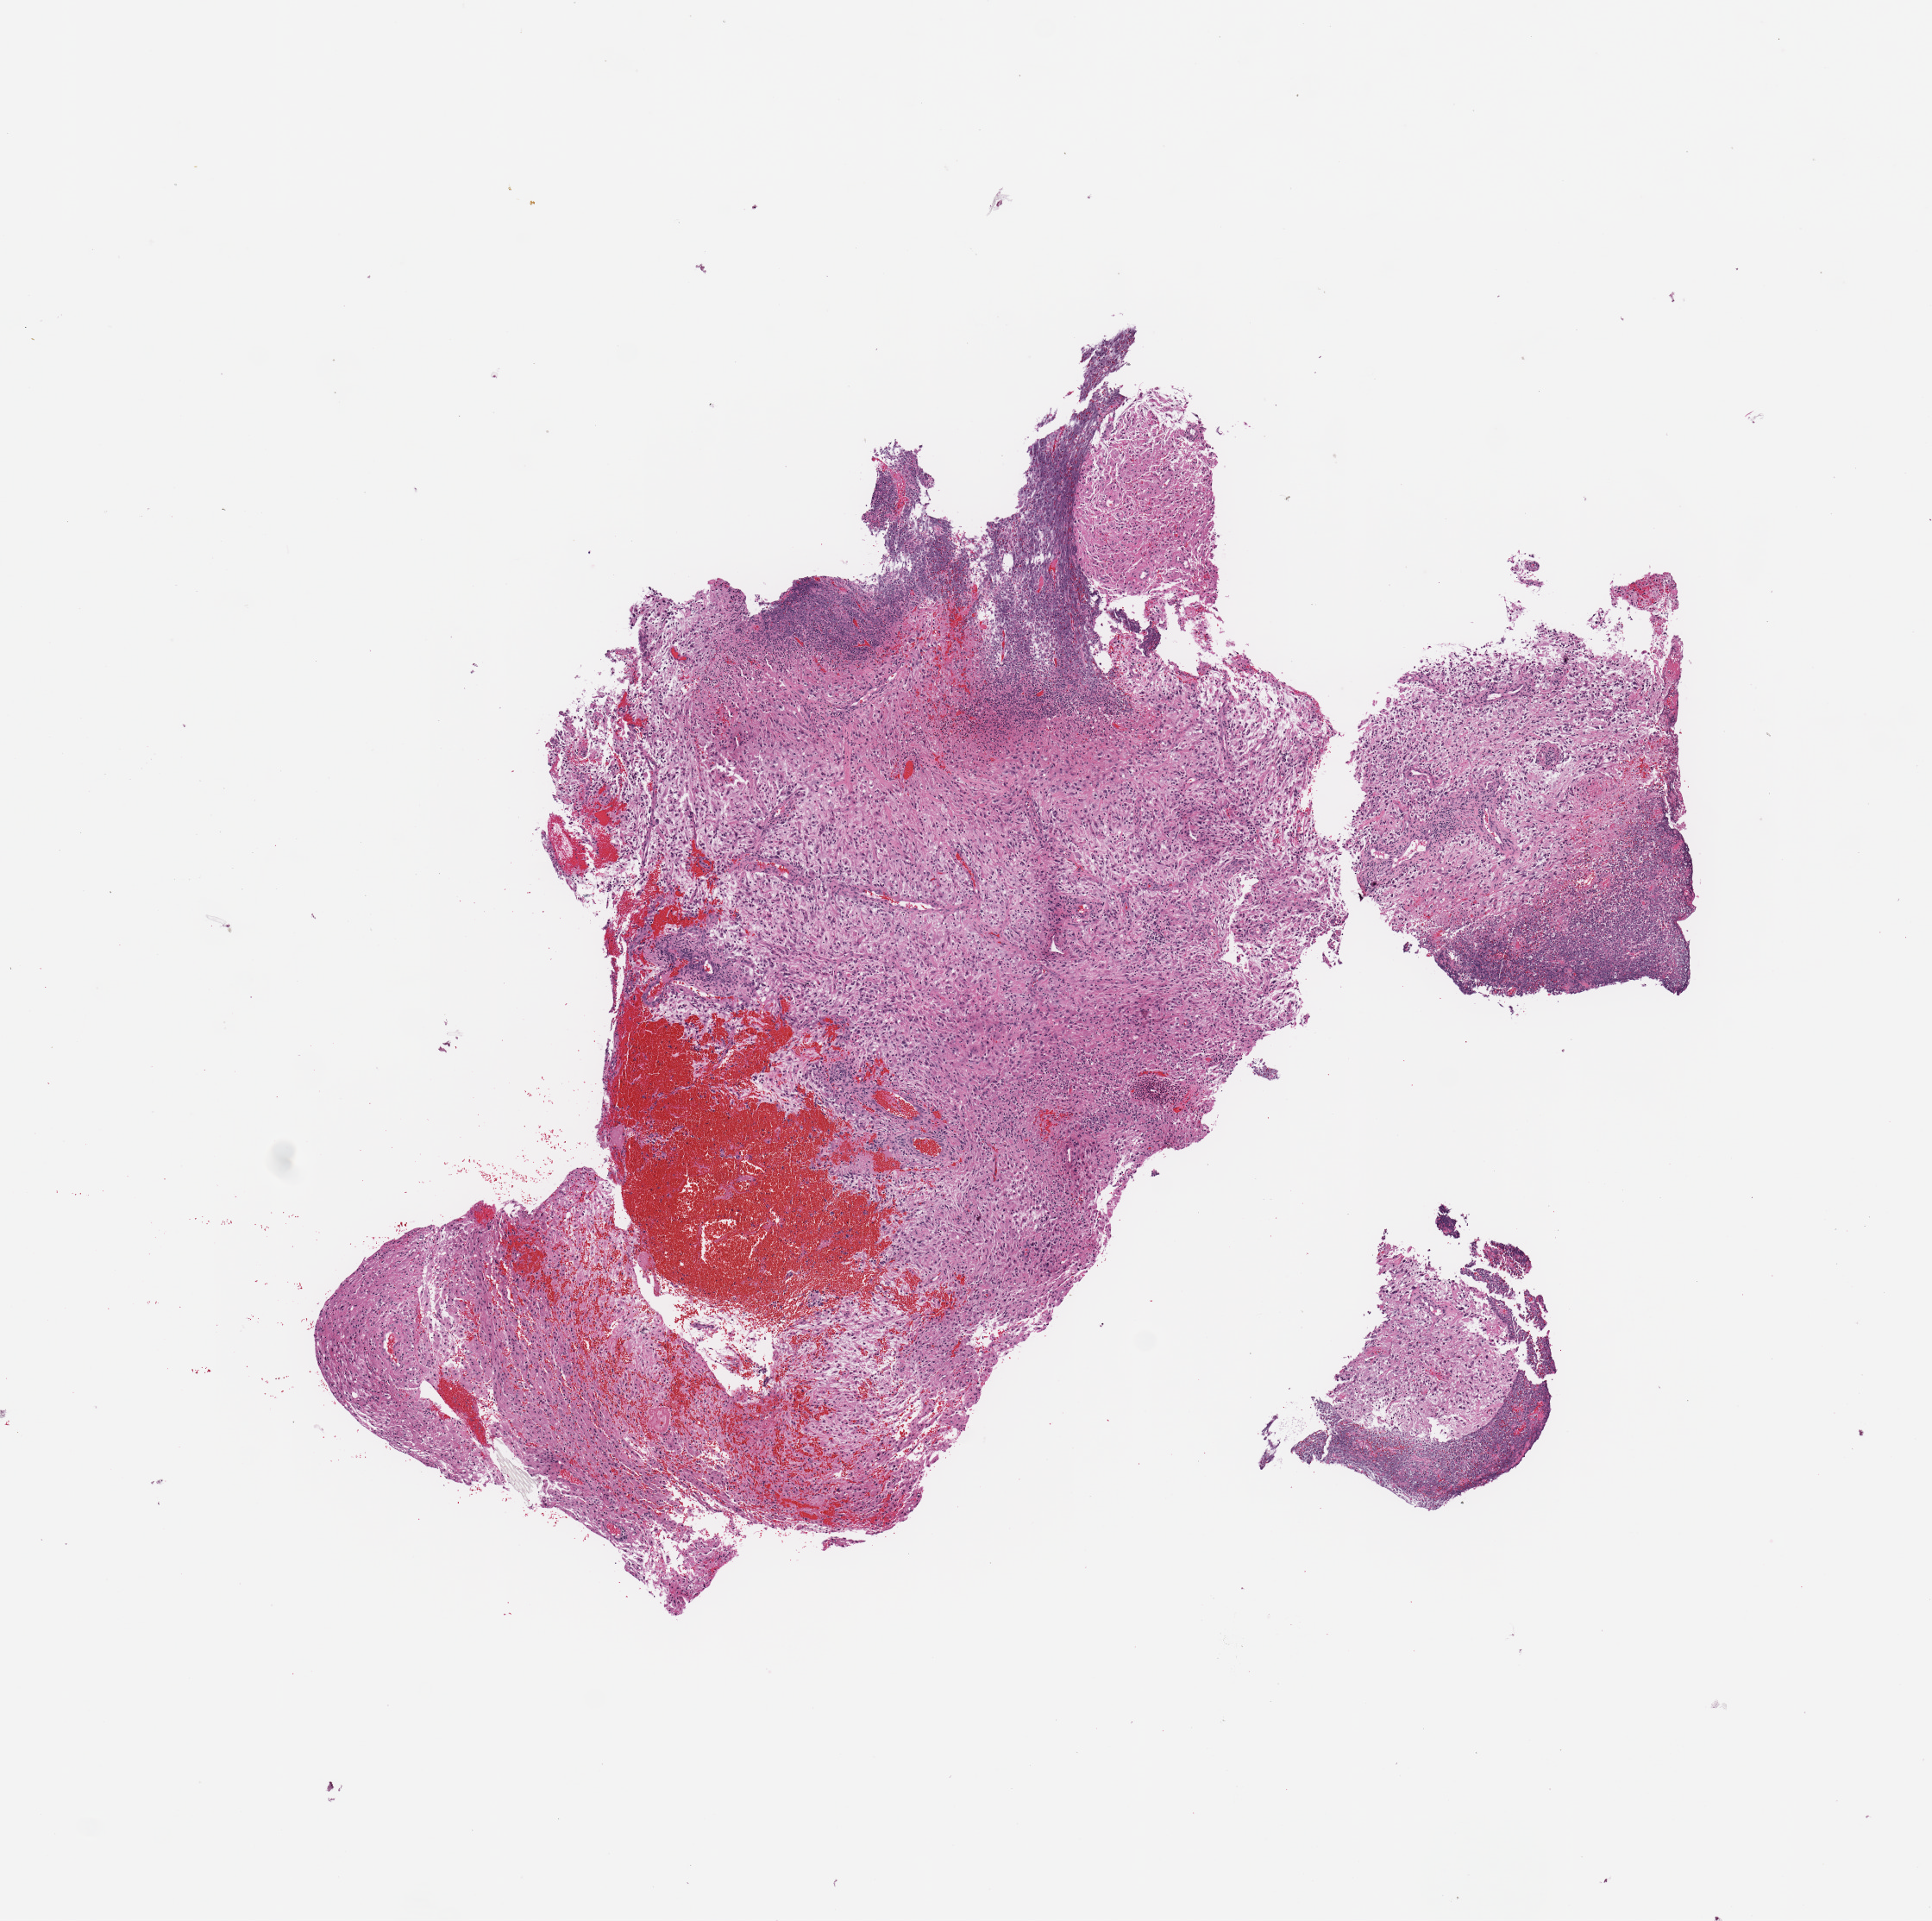
H&E-stained whole-slide image — low-resolution overview of the scanned area, about 8.9 x 8.8 mm (slide scanned at 20x). Tumour tissue sample, sampled site: brain. Female, 50 y/o. Slide review estimates, as recorded: tumour nuclei 70%, necrosis 15%.
• diagnosis: Glioblastoma